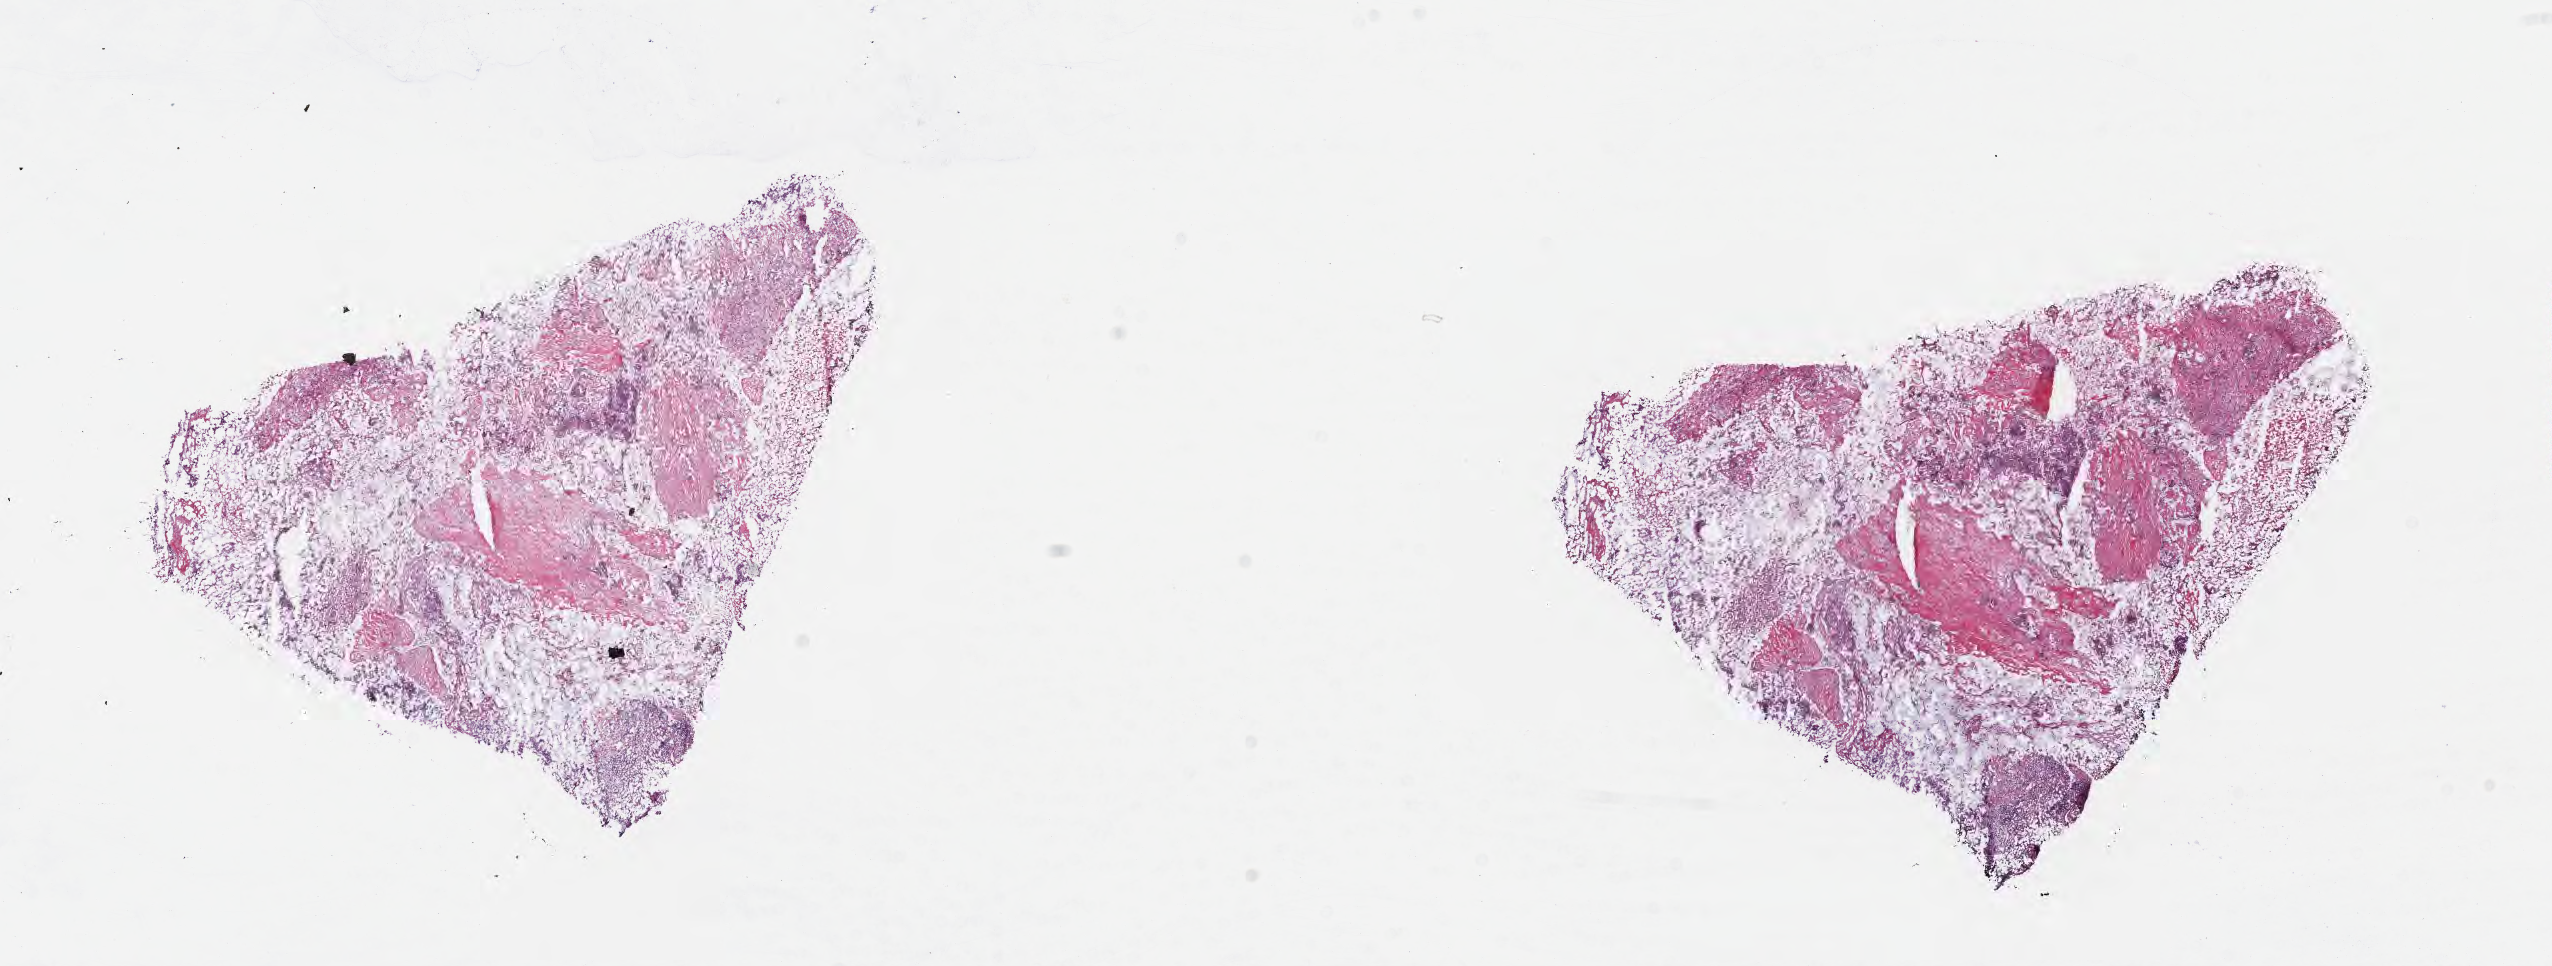
Whole-slide image, hematoxylin and eosin (H&E) stain, whole scanned area (about 20.6 x 7.8 mm) shown as a low-resolution overview. Cryosection. Specimen: metastatic tumor tissue, resected from liver. Patient: female, age at initial diagnosis 51 years. Composition of this section per pathologist review: tumor cells 47%, tumor nuclei 90%, stromal cells 30%, necrosis 20%, normal cells 3%. Inflammatory infiltration, as recorded: lymphocyte infiltration 5%, monocyte infiltration 1%, neutrophil infiltration 0%.
Patient diagnosis (primary): Adenocarcinoma, NOS.